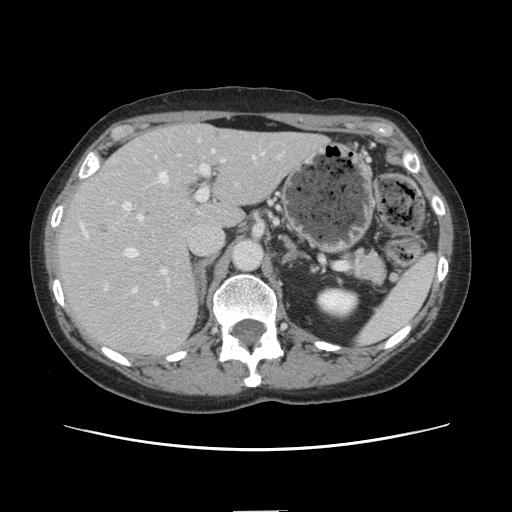
Contrast-enhanced abdominal CT, one axial slice; position 88 of 141 along the scan axis; 120 kVp; intravenous contrast given; soft-tissue window (W 400 / L 40 HU); 2.5 mm slice thickness; 512 × 512 image matrix, field of view 350 × 350 mm. Female patient, age 63 years. Case-level facts recorded for this patient, not image findings: diagnosis: colorectal cancer liver metastases, imaged before liver resection; multiple liver metastases: yes; largest metastasis: 3.2 cm; disease in both lobes: yes.
Outlined on this slice (manually delineated by an expert):
- hepatic veins: bounding box <105,150,255,305> (left, top, right, bottom; pixels)
- liver: <57,125,326,356>
- planned liver remnant (the part of the liver to remain after resection): <178,125,327,228>
- portal vein (with intrahepatic branches): <121,153,227,292>